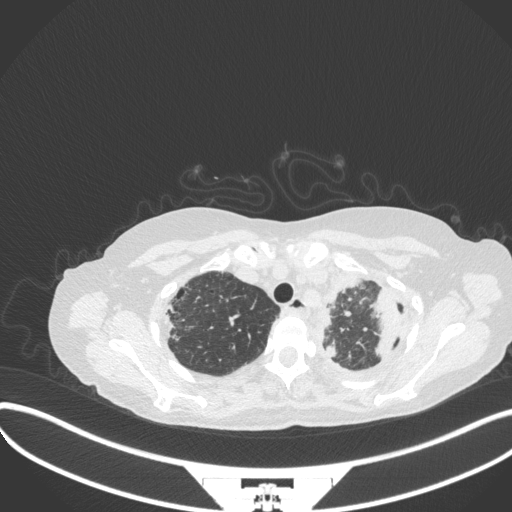
Chest CT, one axial slice. Slice 286 of 373 in the series (ordered by position). Reconstruction kernel B31f. Lung window (W 1500 / L -600 HU). 1 mm slice thickness. 512 × 512 image matrix. Female patient, age 56 years. From the clinical record (not read from this slice): clinical TNM (as recorded): T1 N0 M0.
Annotated regions visible in this slice (bounding box drawn by a radiologist):
- lung tumour (recorded histology: adenocarcinoma): bounding box [x1, y1, x2, y2] px = [370, 281, 404, 358]